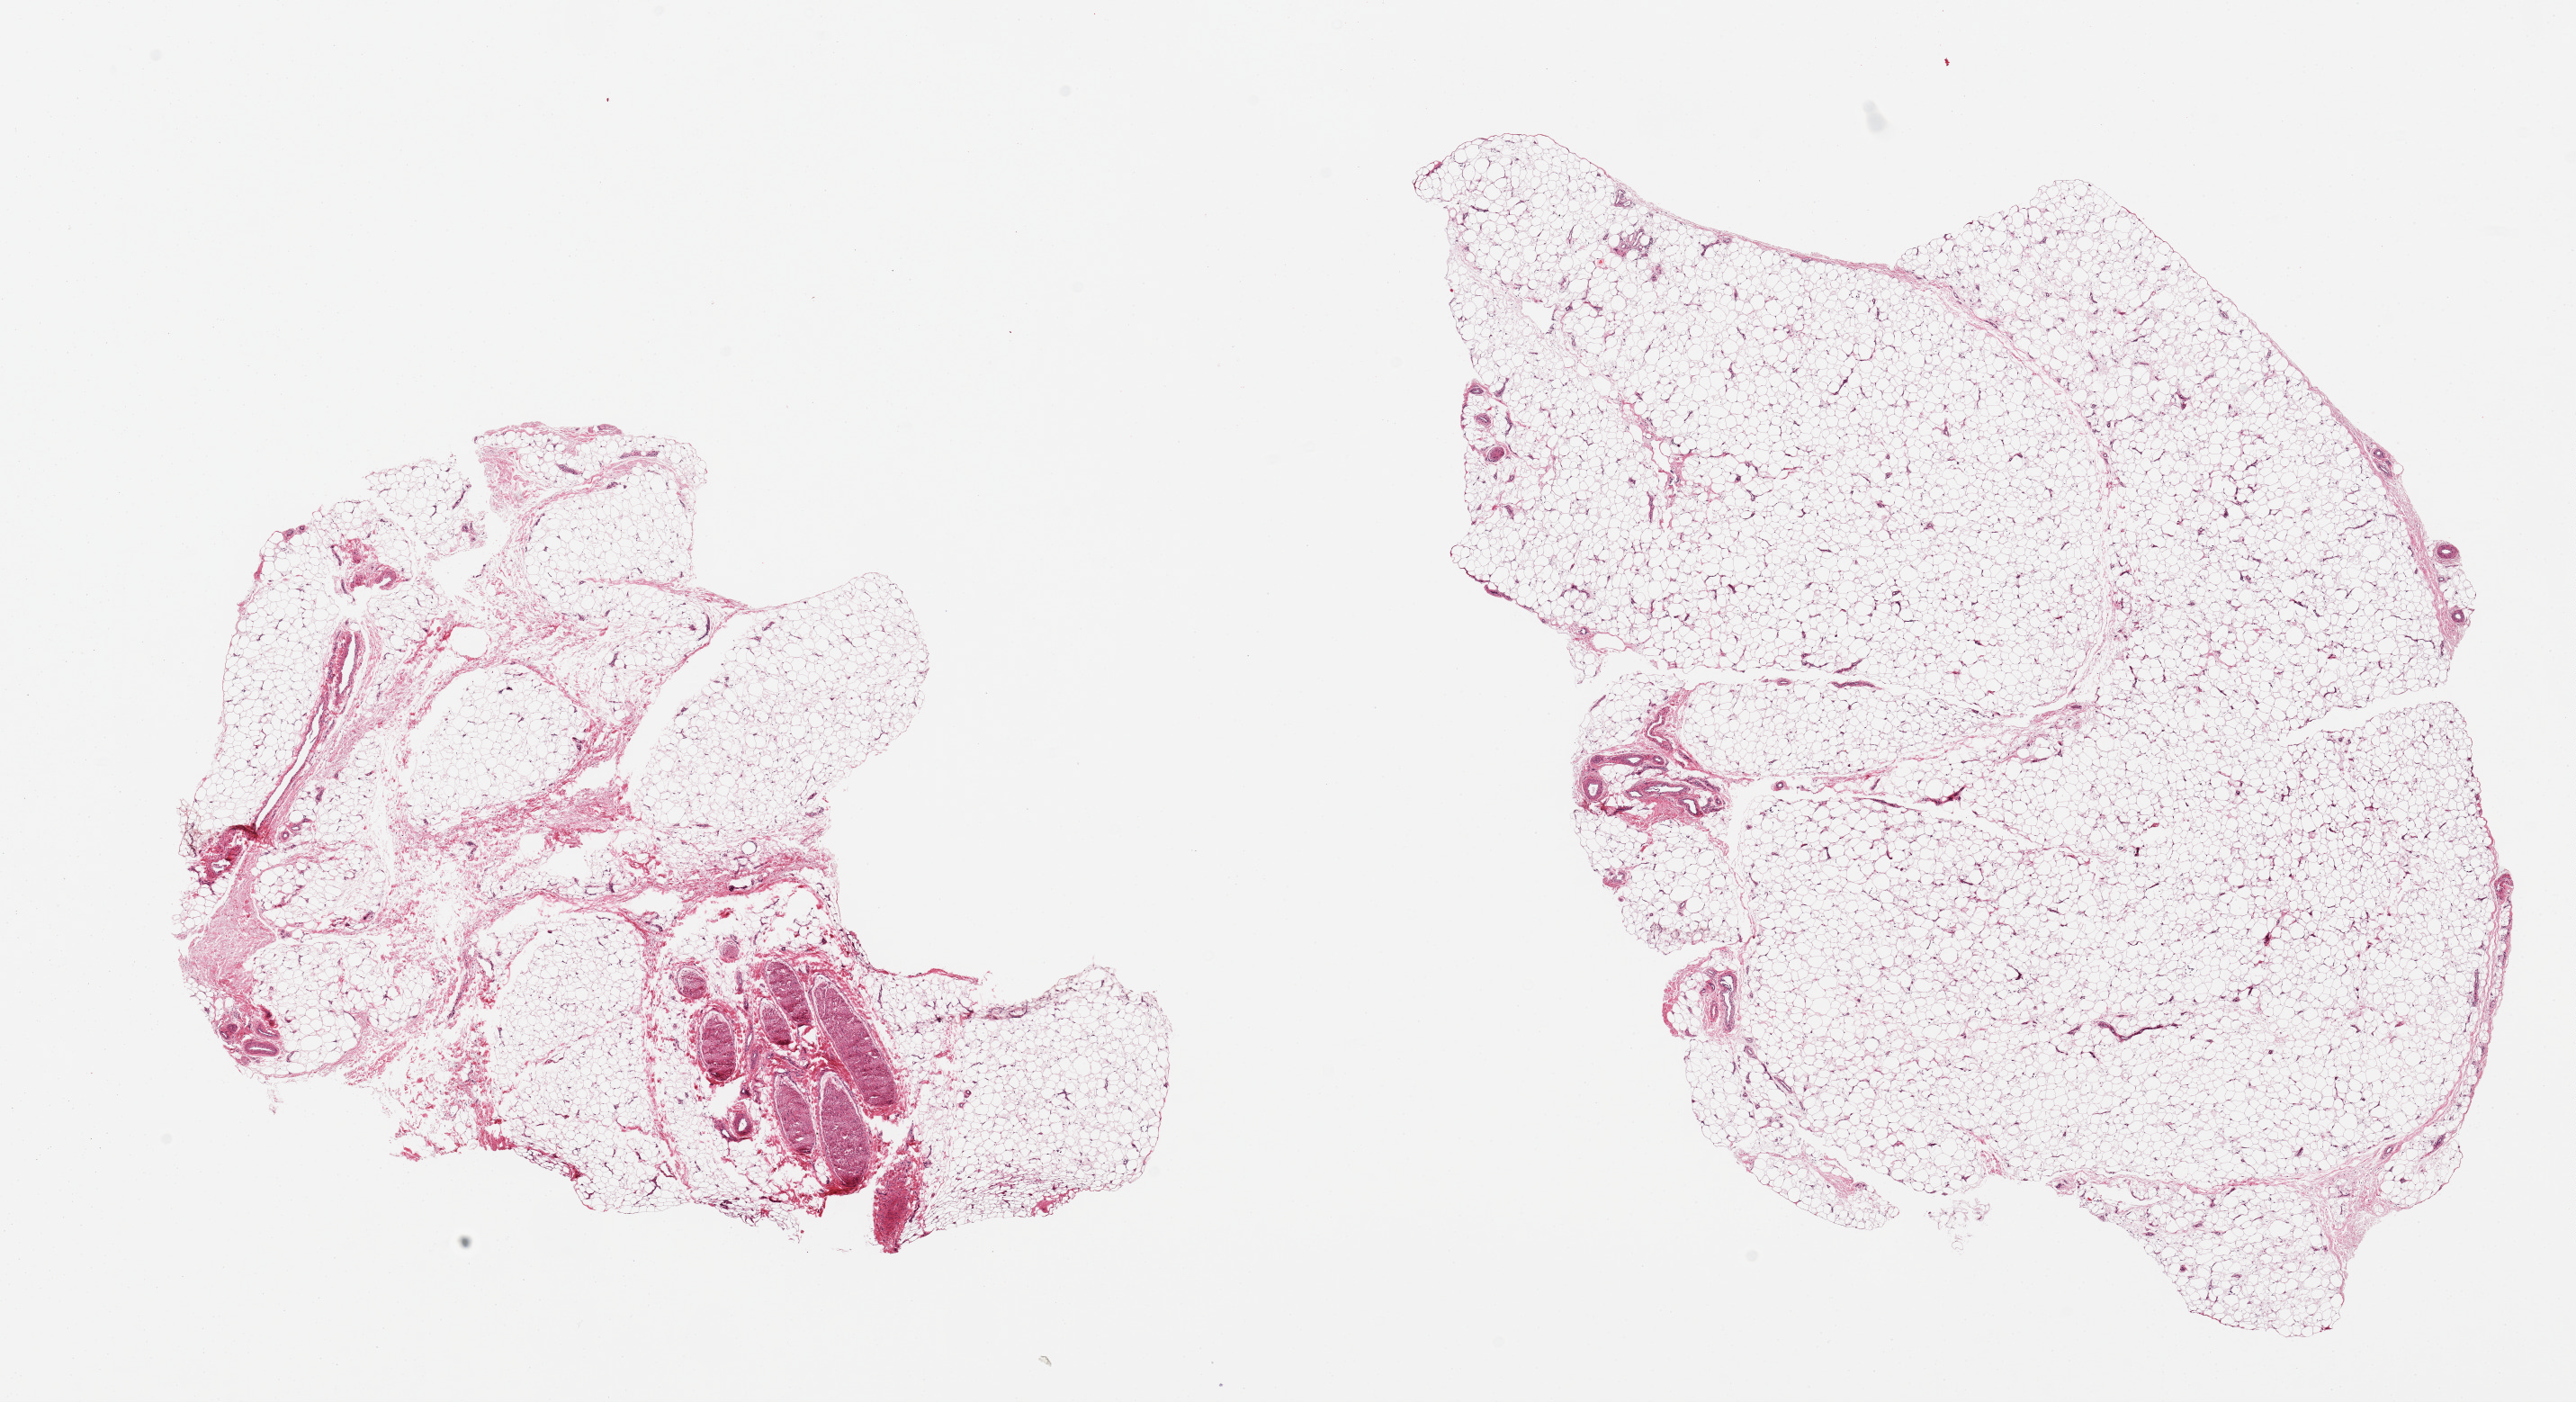
Digitized haematoxylin and eosin-stained section, a low-resolution overview of the entire scanned area, about 22.6 x 12.3 mm (acquisition: 20x scan). PAXgene-fixed paraffin-embedded (PFPE) section. Section of adipose tissue (target tissue). Tissue donor sample. Female donor.
- reviewer comment on this tissue sample: 2 pieces peripheral nerve twigs/vascular elements are ~10% of tissue